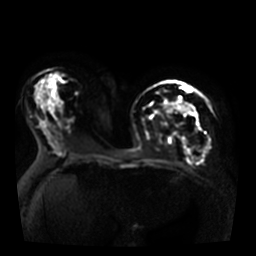
Breast MRI, one axial slice. Position 18 of 36 along the scan axis. Diffusion-weighted series; image 2 of 4 stored at this slice position (different b-values; order by instance number). 3 T. 5 mm slice thickness. 256 × 256 image matrix. Female patient.
Outlined on this slice (manually delineated by an expert):
- tumour on diffusion-weighted imaging: bounding box <182,103,191,113> (left, top, right, bottom; pixels)